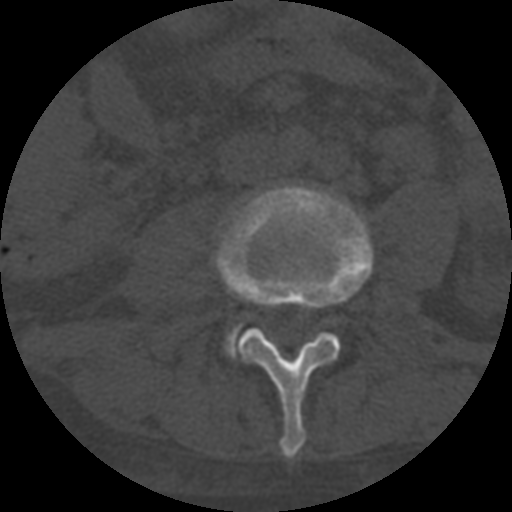
CT including the spine, one axial slice; slice 225 of 708 in the series (ordered by position); 120 kVp; one of 3 acquisitions stored at this slice position; bone window (W 1800 / L 400 HU); 1.25 mm slice thickness; 512 × 512 image matrix, field of view 160 × 160 mm. Patient age 55 years. Case-level facts recorded for this patient, not image findings: primary cancer: colon; vertebrae with lytic lesions (as recorded): T12, L1, L5.
Structures marked on this image (semi-automatic segmentation, software-assisted and operator-edited):
- L3 vertebra: box from (x=216, y=185) to (x=373, y=458) px
- L4 vertebra: (x=225, y=327)–(x=238, y=353)